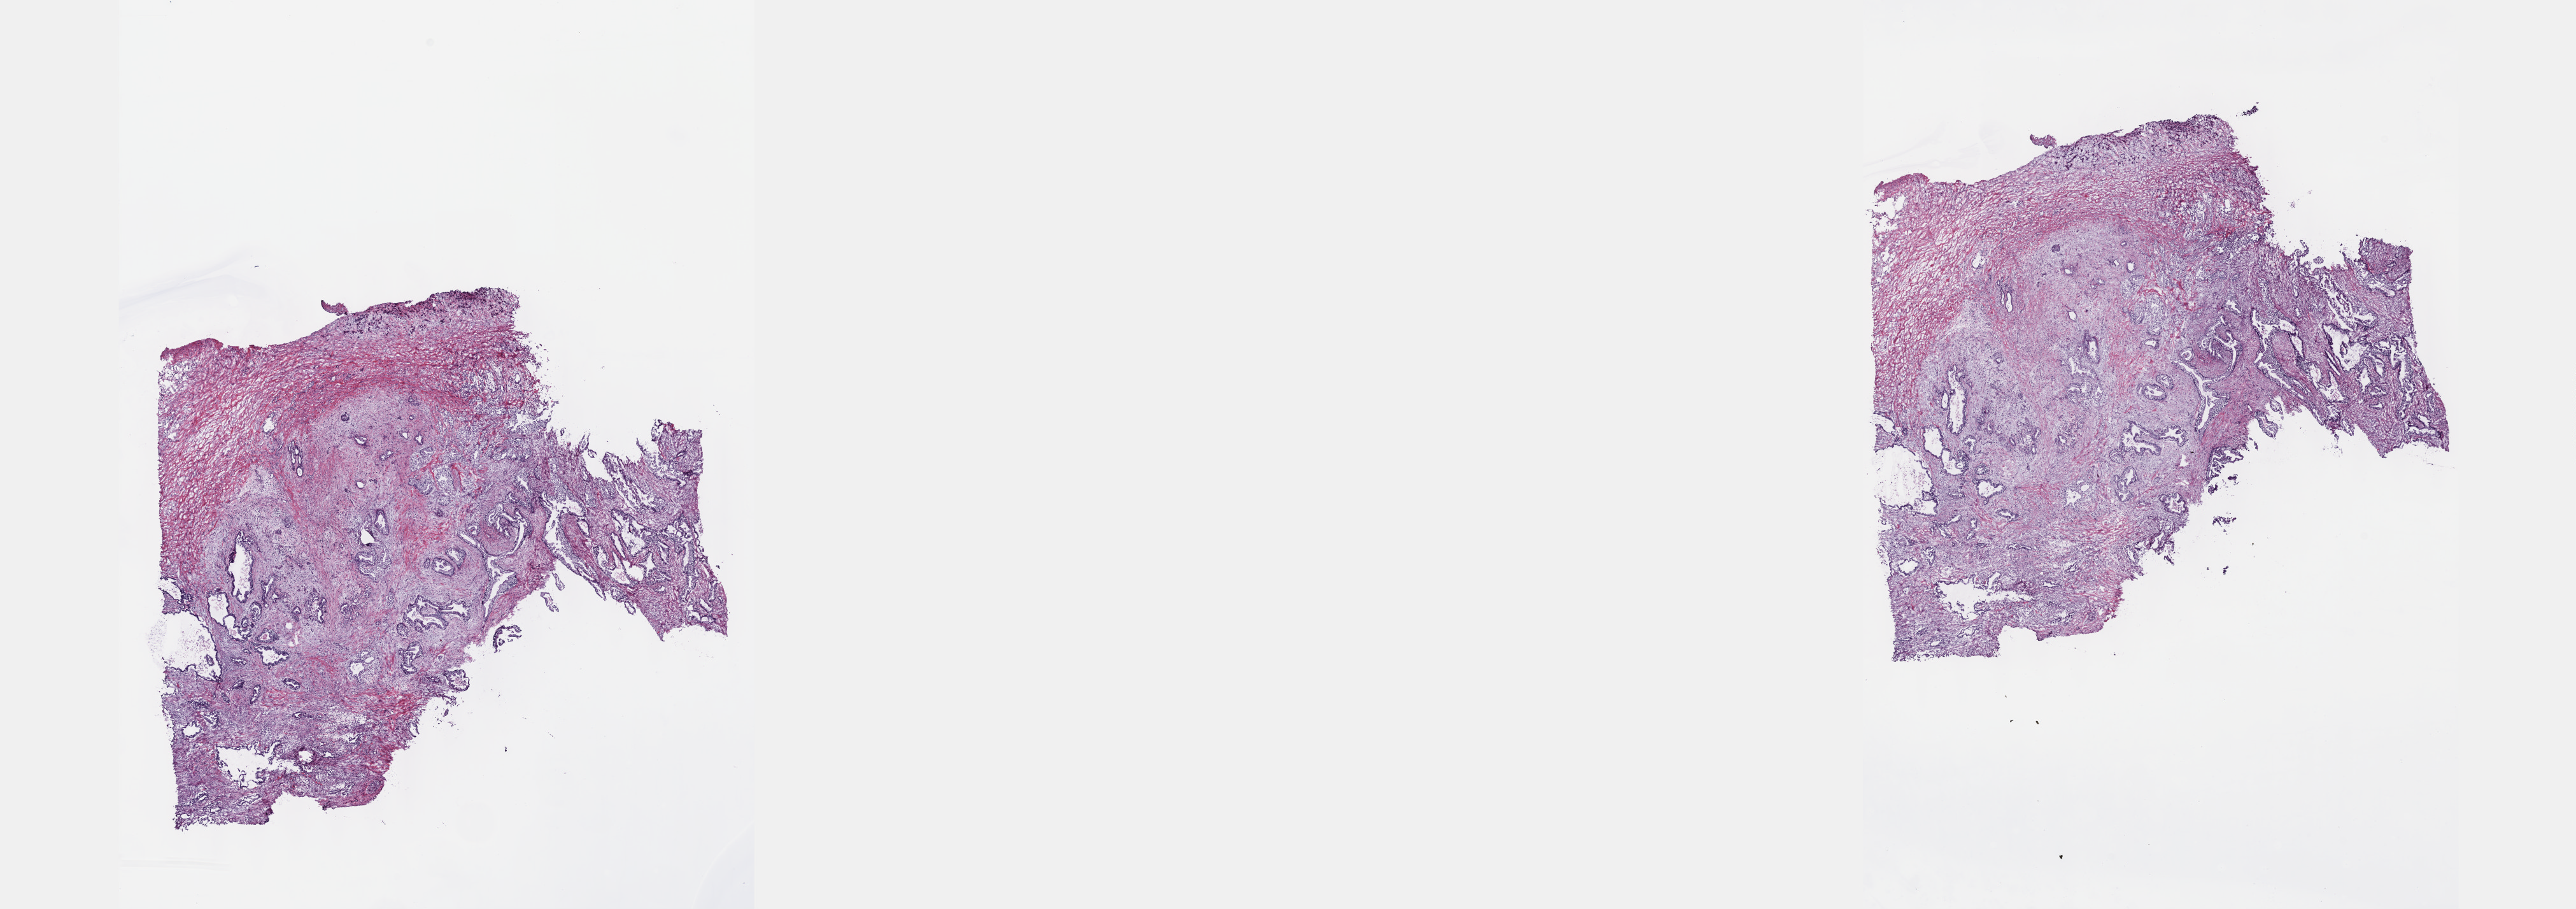
Whole-slide histology image, Hematoxylin and eosin (H&E) stained, a low-resolution overview of the entire scanned area, about 32.7 x 11.5 mm, frozen section from the top of the tissue portion, primary tumour sample from the pancreas. Patient: male, age at initial diagnosis 73 years. Histologic grade: G2 (moderately differentiated). Composition of this section per pathologist review: tumour cells 15%, tumour nuclei 15%, normal cells 20%, stromal cells 65%, necrosis 0%. Inflammatory infiltration, as recorded: lymphocyte infiltration 4%, monocyte infiltration 2%, neutrophil infiltration 9%.
Lymph nodes positive (case pathology): 0 of 24 examined. Histologic diagnosis: Infiltrating duct carcinoma, NOS (body of pancreas). TNM: T3 N0 M0. AJCC pathologic stage: IIA (7th edition).